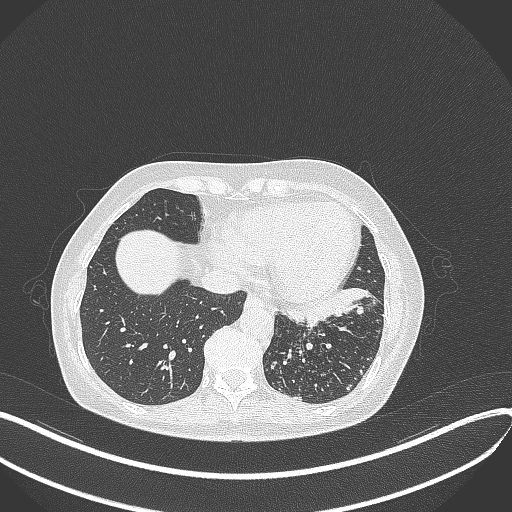
Chest CT, one axial slice; position 117 of 429 along the scan axis; lung window (W 1500 / L -600 HU); 1 mm slice thickness; 512 × 512 image matrix, field of view 400 × 400 mm. Patient: female, 63 years. Case-level facts recorded for this patient, not image findings: clinical TNM (as recorded): T1b N0 M0.
Structures marked on this image (rectangle marked by the reading radiologist):
- lung tumour (recorded histology: adenocarcinoma): bounding box [x1, y1, x2, y2] px = [284, 285, 376, 326]